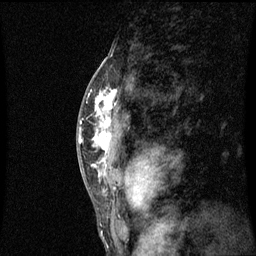
Breast MRI (dynamic contrast-enhanced), one sagittal slice; slice 39 of 60 in the series (ordered by position); dynamic contrast-enhanced series, image 2 of 3 at this slice position (ordered by acquisition); 1.5 T; TE 4.2 ms, TR 8.9 ms; 2 mm slice thickness; 256 × 256 image matrix, field of view 200 × 200 mm. Female patient, age 50 years. From the clinical record (not read from this slice): setting: breast cancer imaged before/during neoadjuvant chemotherapy; receptor status: triple-negative.
Outlined on this slice (semi-automatically segmented with operator editing):
- analysis volume of interest (the breast-tissue region the enhancement analysis was run in; not a lesion): bounding box (x1, y1, x2, y2) in pixels: (84, 80, 127, 171)
- tumour enhancement mask (voxels above the 70 % enhancement threshold inside the analysis volume of interest): (92, 90, 117, 167)